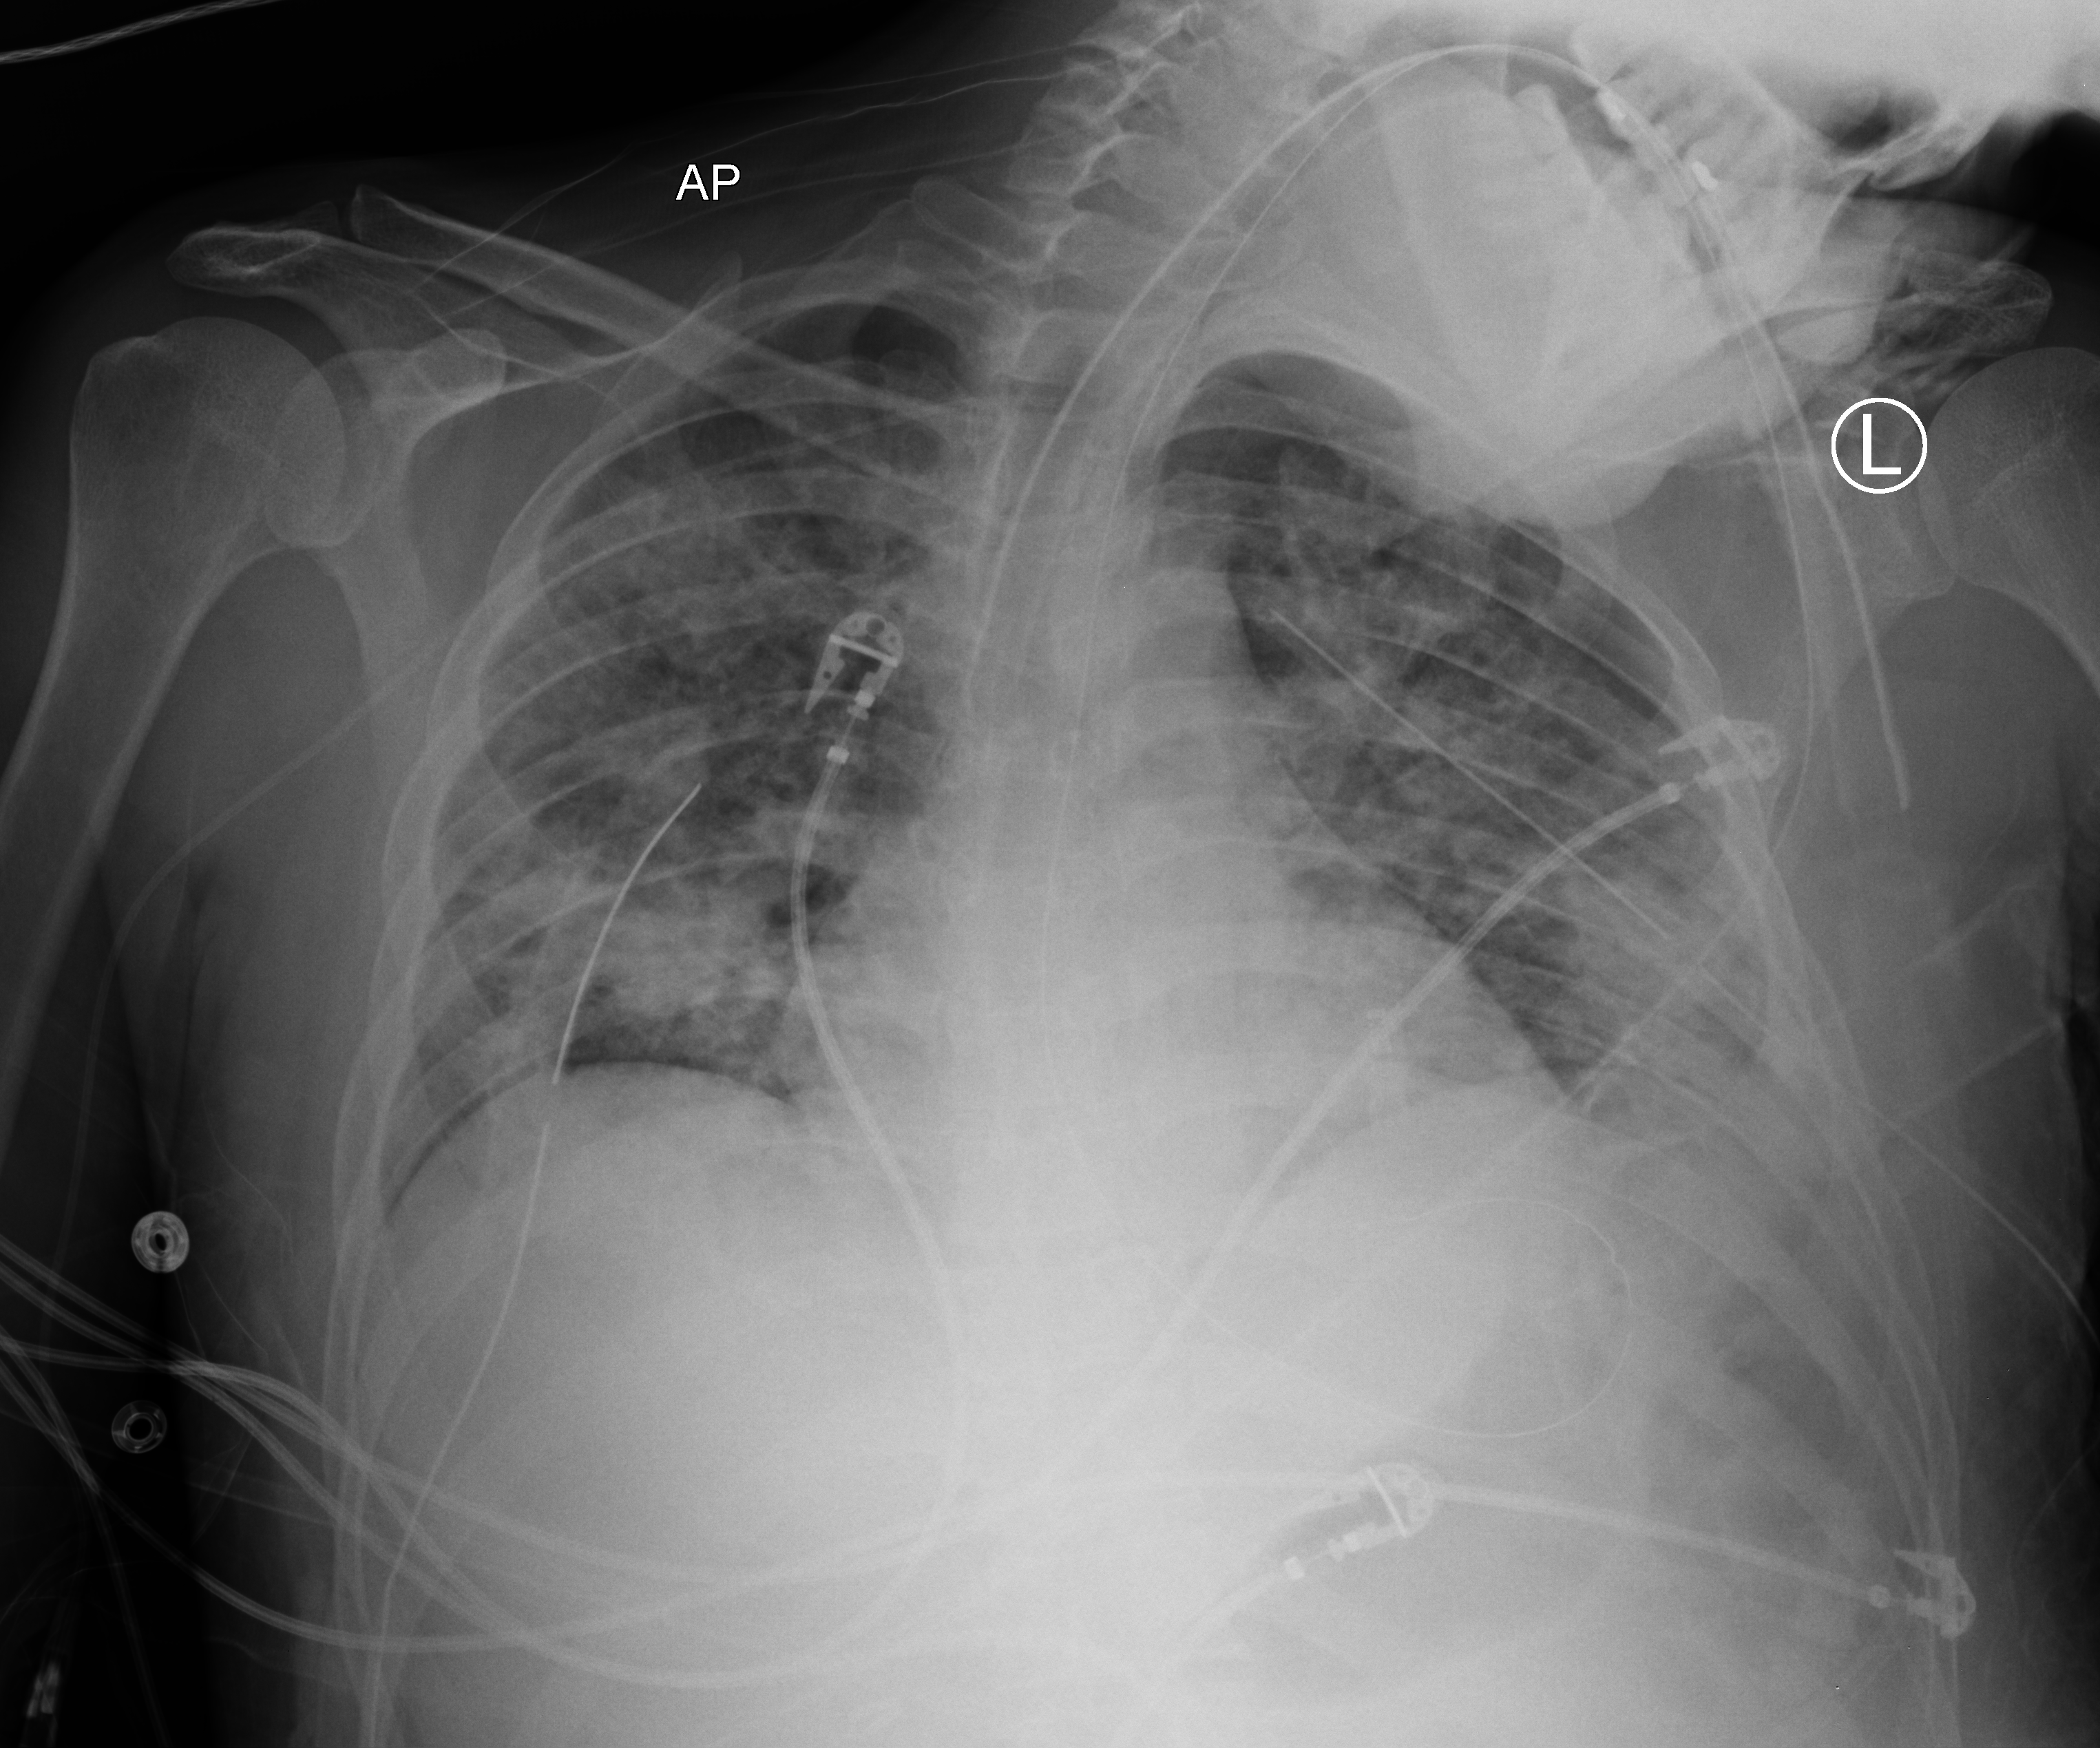
Portable chest radiograph; anteroposterior (AP) projection. Male patient hospitalised with COVID-19, age 18–59 years.
Hospital-stay facts (about this admission, not read from this image; timing relative to this image not recorded): admitted to intensive care during this hospital stay: yes; length of hospital stay: 29 days; COPD (admission record): no.